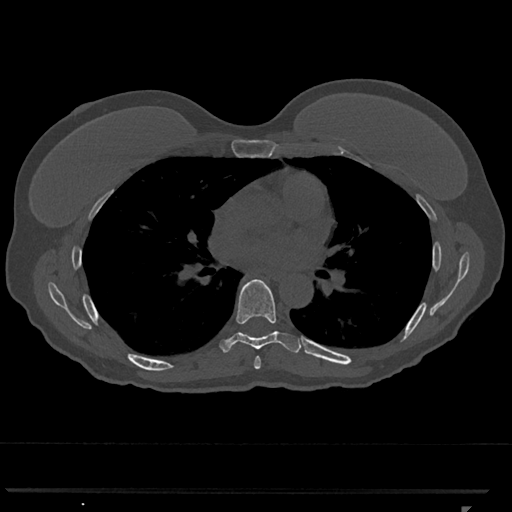
CT including the spine, one axial slice; slice 714 of 793 in the series (ordered by position); reconstruction kernel Br40s/3; bone window (W 1800 / L 400 HU); 0.5 mm slice thickness; 512 × 512 image matrix, field of view 380 × 380 mm. Patient: female, 62 years. Case-level facts recorded for this patient, not image findings: primary cancer: renal.
Annotated regions visible in this slice (semi-automatic segmentation, software-assisted and operator-edited):
- T6 vertebra: bounding box [x1, y1, x2, y2] px = [254, 356, 261, 369]
- T7 vertebra: [220, 279, 302, 353]